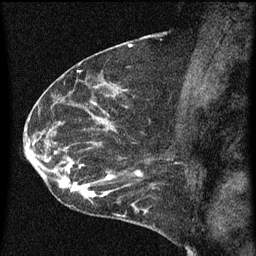
Breast MRI (dynamic contrast-enhanced), one sagittal slice. Position 38 of 60 along the scan axis. Dynamic contrast-enhanced series, image 2 of 3 at this slice position (ordered by acquisition). 1.5 T. TE 4.2 ms, TR 8 ms. 2 mm slice thickness. 256 × 256 image matrix, field of view 180 × 180 mm. Female patient, age 54 years.
Outlined on this slice (semi-automatically segmented with operator editing):
- analysis volume of interest (the breast-tissue region the enhancement analysis was run in; not a lesion): bounding box (x1, y1, x2, y2) in pixels: (49, 138, 164, 209)
- tumour enhancement mask (voxels above the 70 % enhancement threshold inside the analysis volume of interest): (49, 142, 154, 209)